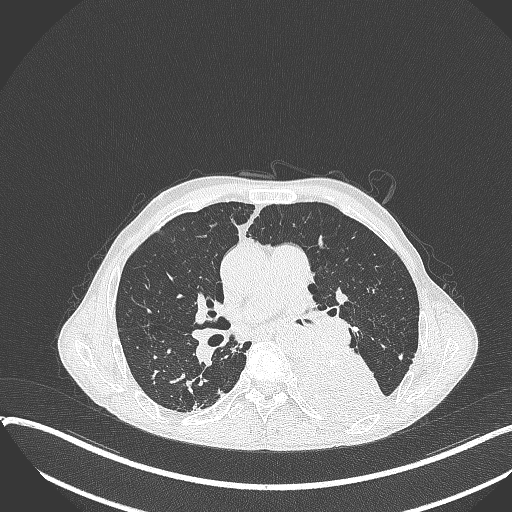
Chest CT, one axial slice. Slice 210 of 401 in the series (ordered by position). Reconstruction kernel B70f. 120 kVp. Lung window (W 1500 / L -600 HU). 512 × 512 image matrix, field of view 400 × 400 mm. Male patient, age 57 years. Case-level facts recorded for this patient, not image findings: clinical TNM (as recorded): T4 N0 M0.
Outlined on this slice (bounding box drawn by a radiologist):
- lung tumour (recorded histology: squamous cell carcinoma): box from (x=290, y=346) to (x=395, y=426) px